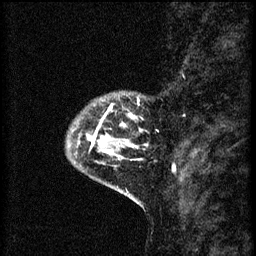
Breast MRI (dynamic contrast-enhanced), one sagittal slice; slice 11 of 60 in the series (ordered by position); 3 images stored at this slice position (order not interpretable as contrast timing); 1.5 T; TE 4.2 ms, TR 8.2 ms; 2 mm slice thickness; 256 × 256 image matrix, field of view 180 × 180 mm. Patient: female, 41 years.
Outlined on this slice (semi-automatic segmentation, software-assisted and operator-edited):
- analysis volume of interest (the breast-tissue region the enhancement analysis was run in; not a lesion): box from (x=67, y=94) to (x=145, y=175) px
- tumour enhancement mask (voxels above the 70 % enhancement threshold inside the analysis volume of interest): (x=78, y=104)–(x=142, y=161)